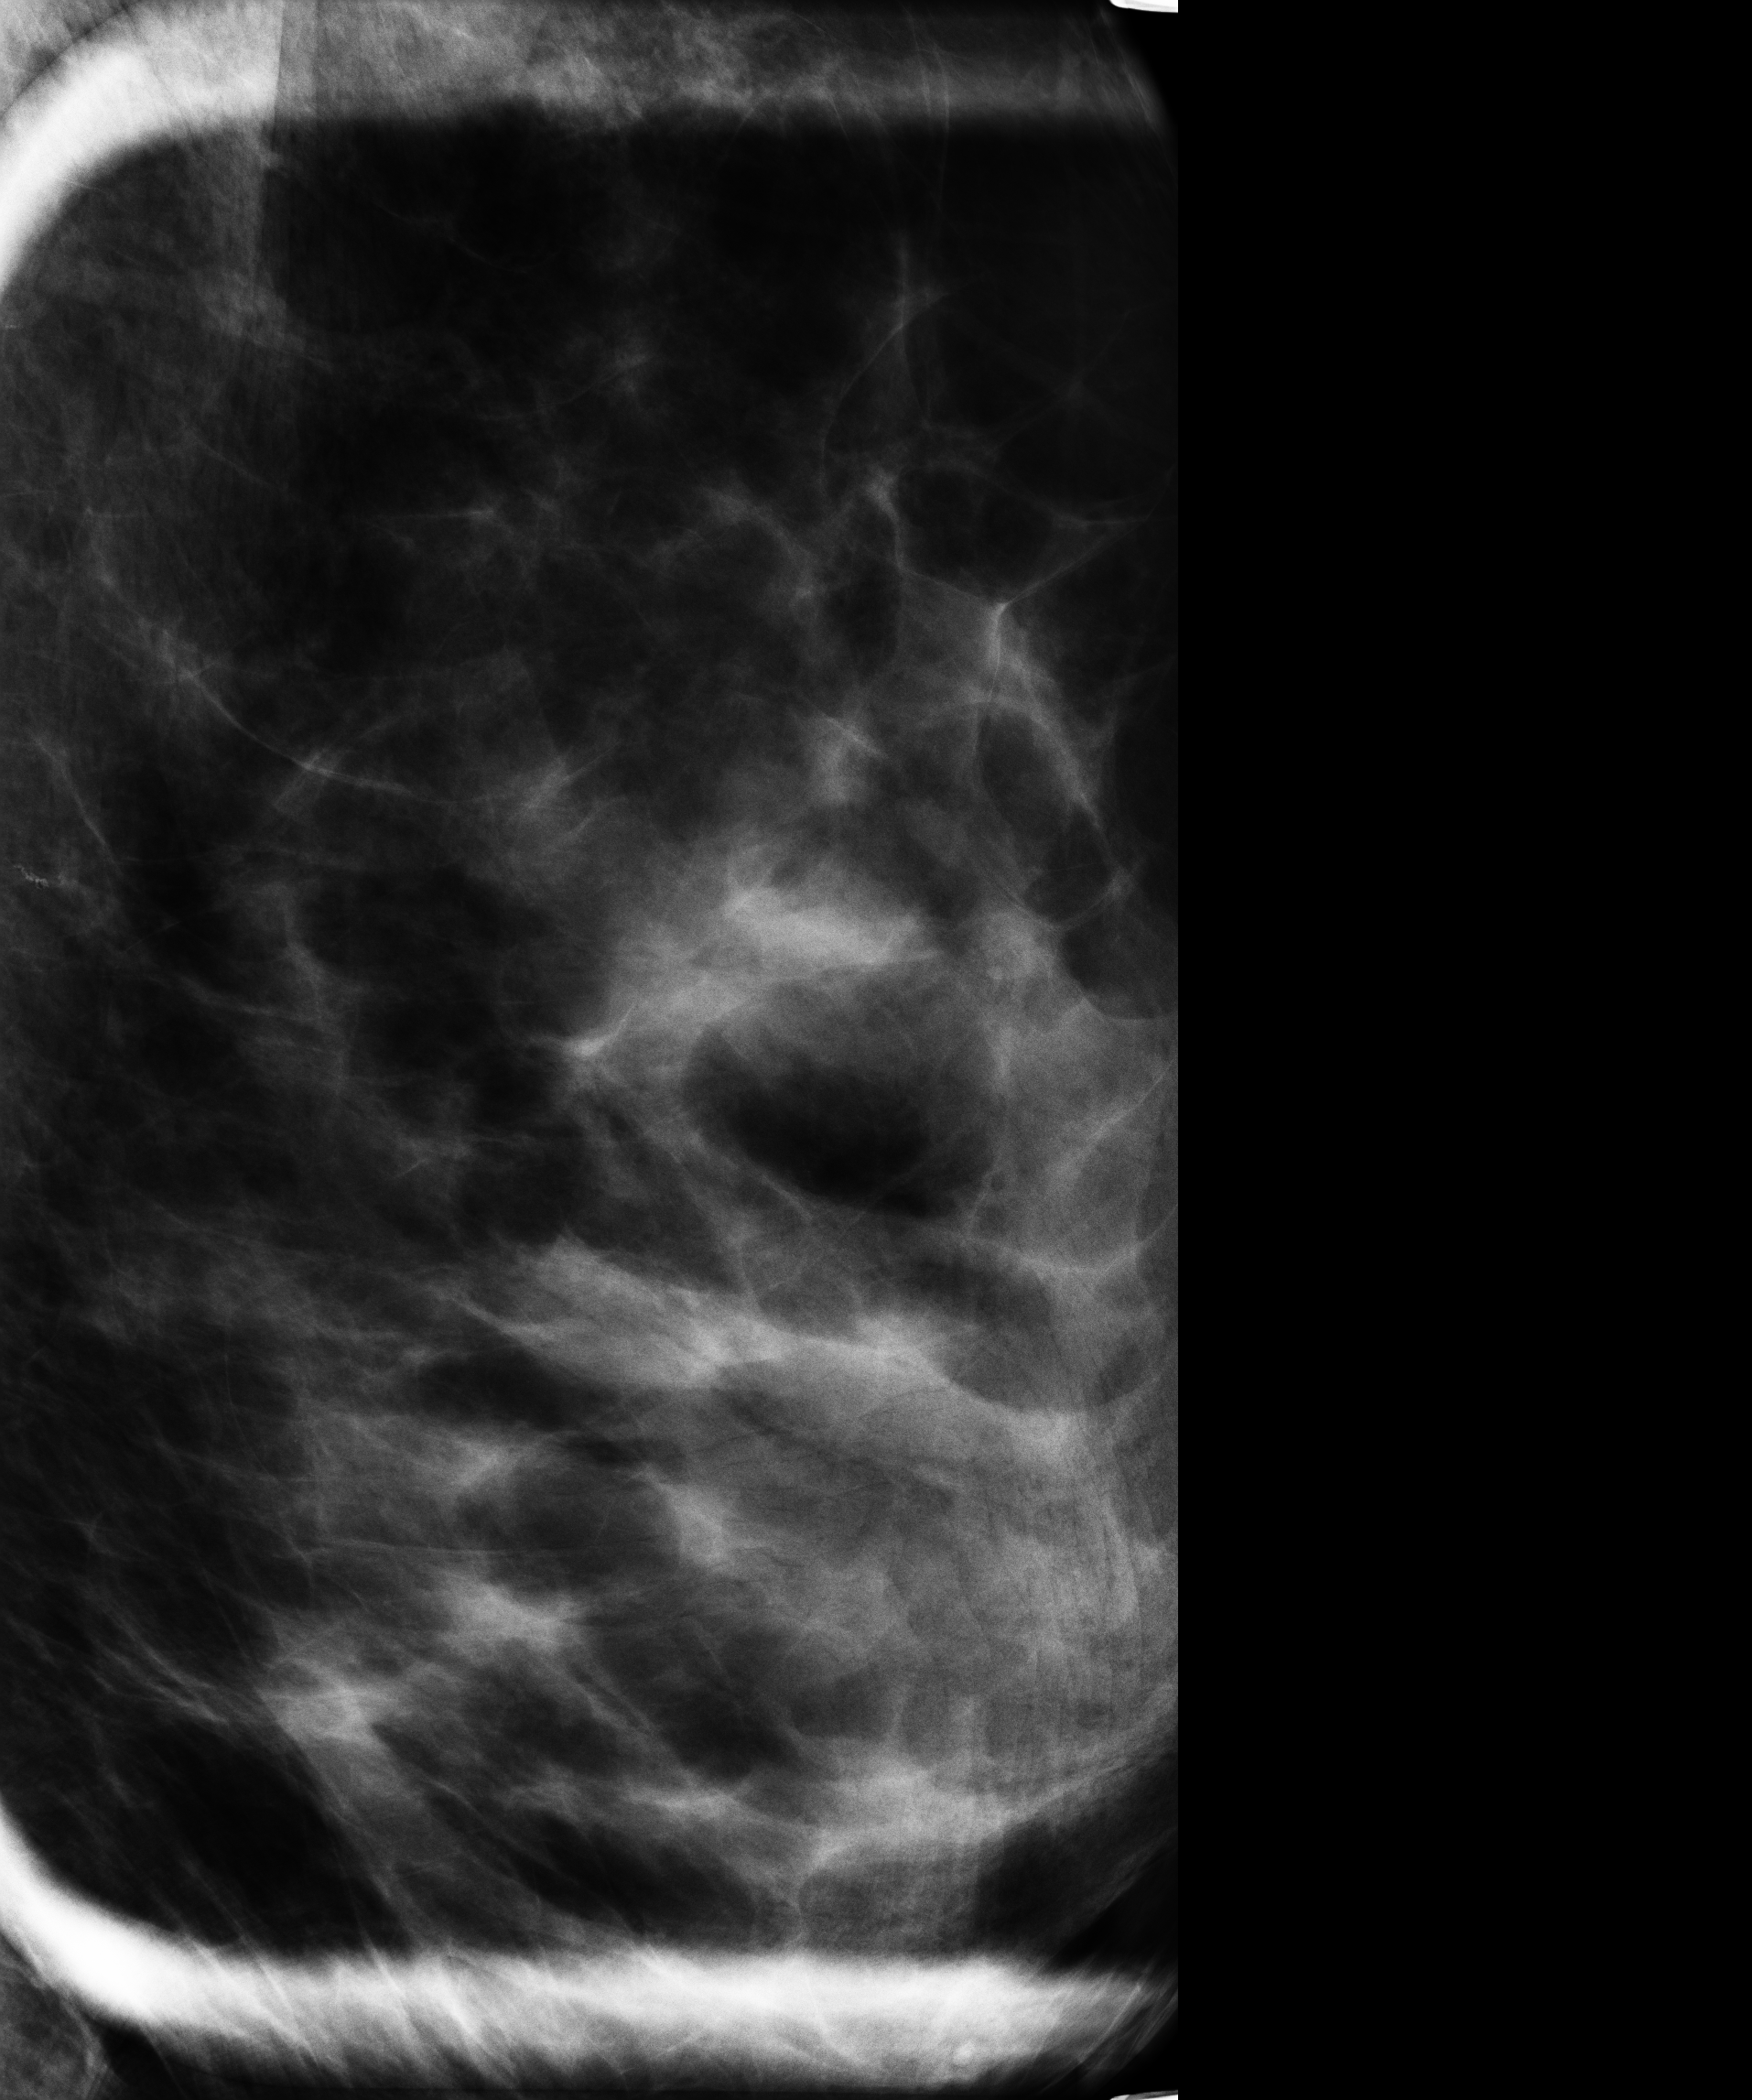
Digital mammogram (FFDM), left breast, ML view, diagnostic examination (additional views), system: Senographe Essential VERSION ADS_54.11. Female patient, age 54 years.
Breast density at the screening exam (both breasts): heterogeneously dense (BI-RADS density category c). Final BI-RADS category for the screening round (tomosynthesis exam, both breasts): category 3. Recall: recalled for additional imaging after this screen.